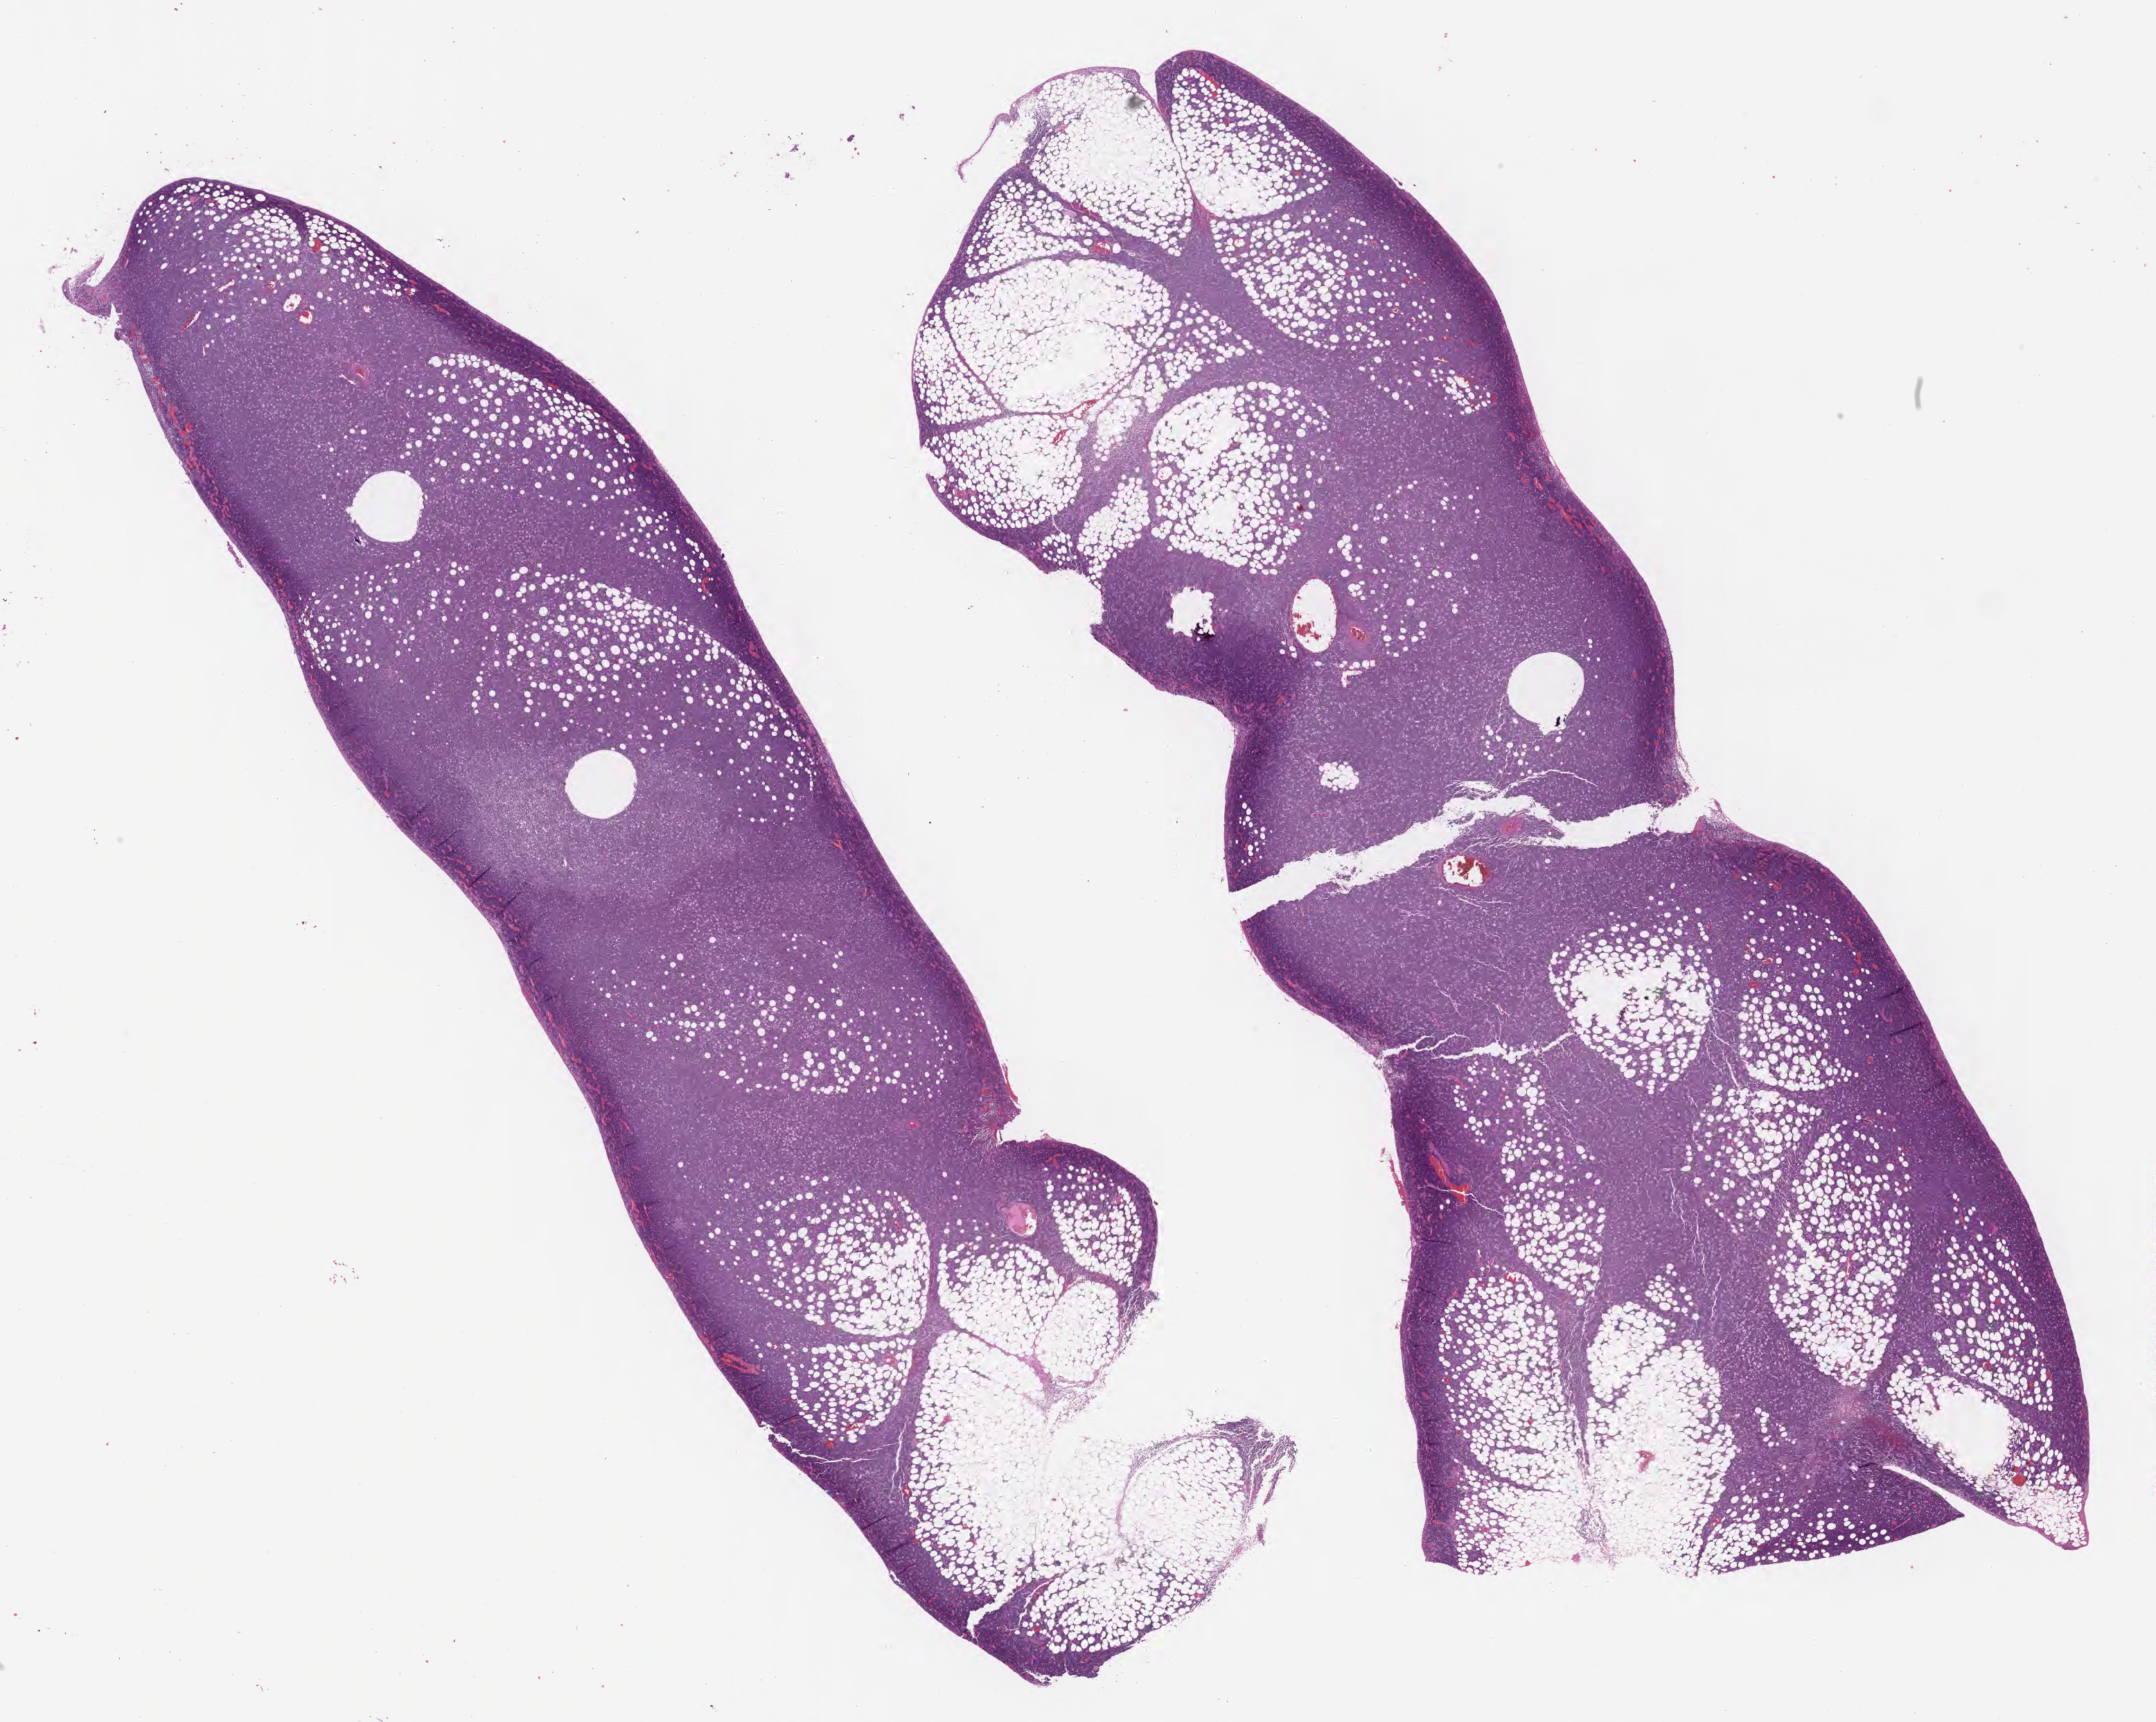
Whole-slide image, H&E stain, low-resolution overview of the scanned area, about 25.2 x 20.1 mm; formalin-fixed, paraffin-embedded (FFPE) tissue; specimen: primary tumor. Patient: male, aged 32. Composition of this section per pathologist review: tumor cells 80%, tumor nuclei 95%, stromal cells 5%, necrosis 5%, normal cells 10%. Inflammatory infiltration, as recorded: lymphocyte infiltration 40%, monocyte infiltration 30%, neutrophil infiltration 5%.
Diagnosis: Burkitt lymphoma, NOS. Ann Arbor stage (patient): Stage IV.